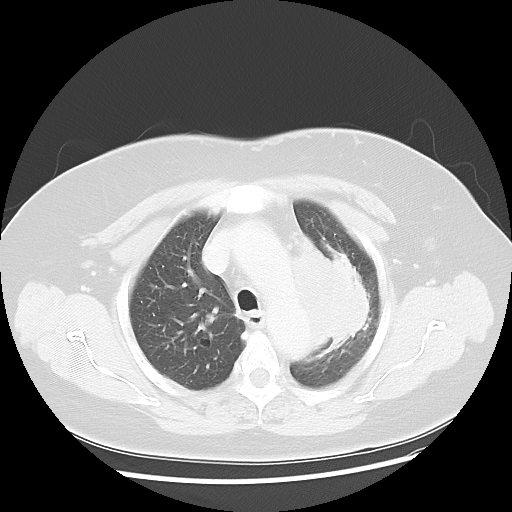
Chest CT, one axial slice. Position 36 of 49 along the scan axis. 120 kVp. Lung window (W 1500 / L -600 HU). 5 mm slice thickness. 512 × 512 image matrix, field of view 374 × 374 mm. Patient: female, 58 years. From the clinical record (not read from this slice): clinical TNM (as recorded): T4 N3 M0.
Outlined on this slice (rectangle marked by the reading radiologist):
- lung tumour (recorded histology: small cell carcinoma): bounding box <292,239,378,354> (left, top, right, bottom; pixels)